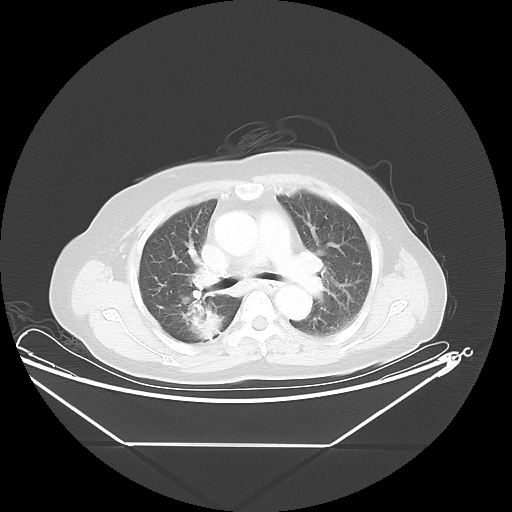
Chest CT, one axial slice; reconstruction kernel LUNG; lung window (W 1500 / L -600 HU); 5 mm slice thickness; 512 × 512 image matrix, field of view 462 × 462 mm. Patient: female, 62 years. Case-level facts recorded for this patient, not image findings: clinical TNM (as recorded): T1c N0 M0; histopathological grade: G2-3.
Annotated regions visible in this slice (bounding box drawn by a radiologist):
- lung tumour (recorded histology: adenocarcinoma): bounding box <182,300,225,347> (left, top, right, bottom; pixels)